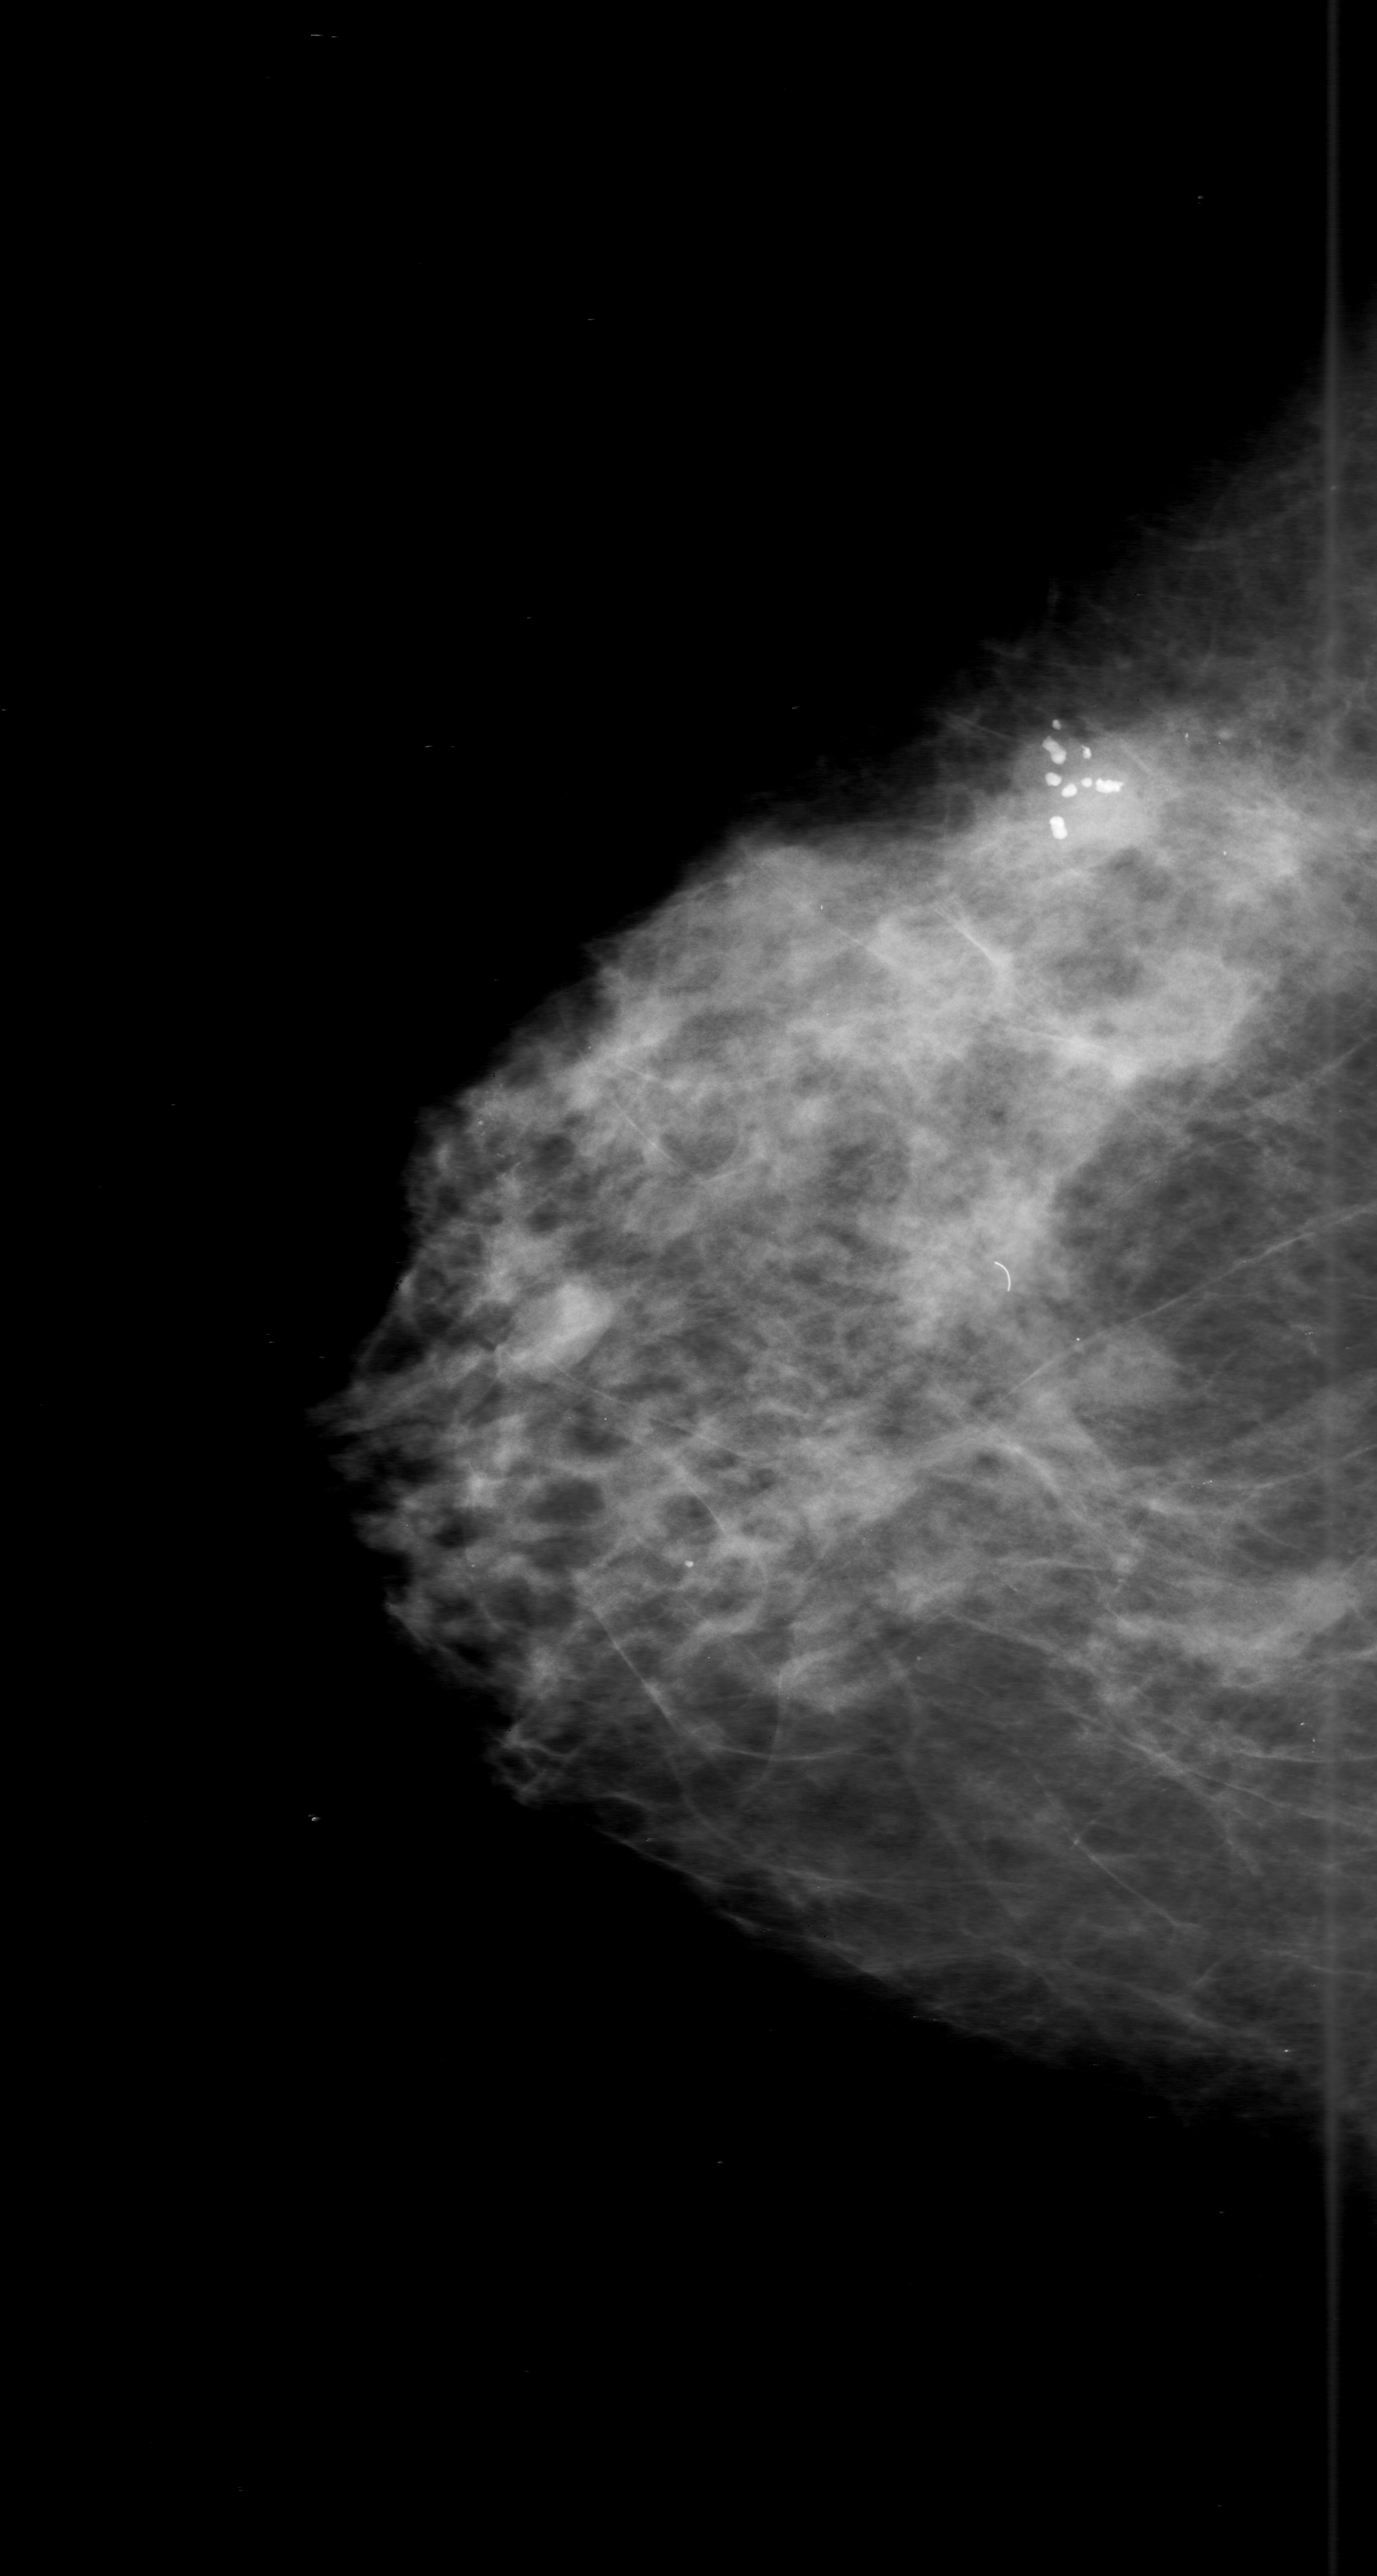
Scanned film-screen mammogram. Right breast. Craniocaudal (CC) view. BI-RADS breast density category 3 (scale 1–4). 1377 × 2576 image matrix.
Expert-marked regions of interest on this film, with their recorded descriptors:
- calcifications, morphology punctate / fine linear branching, distribution clustered; BI-RADS assessment category 0; pathology result (as recorded, not read from the image): malignant: bounding box <357,964,699,1287> (left, top, right, bottom; pixels)